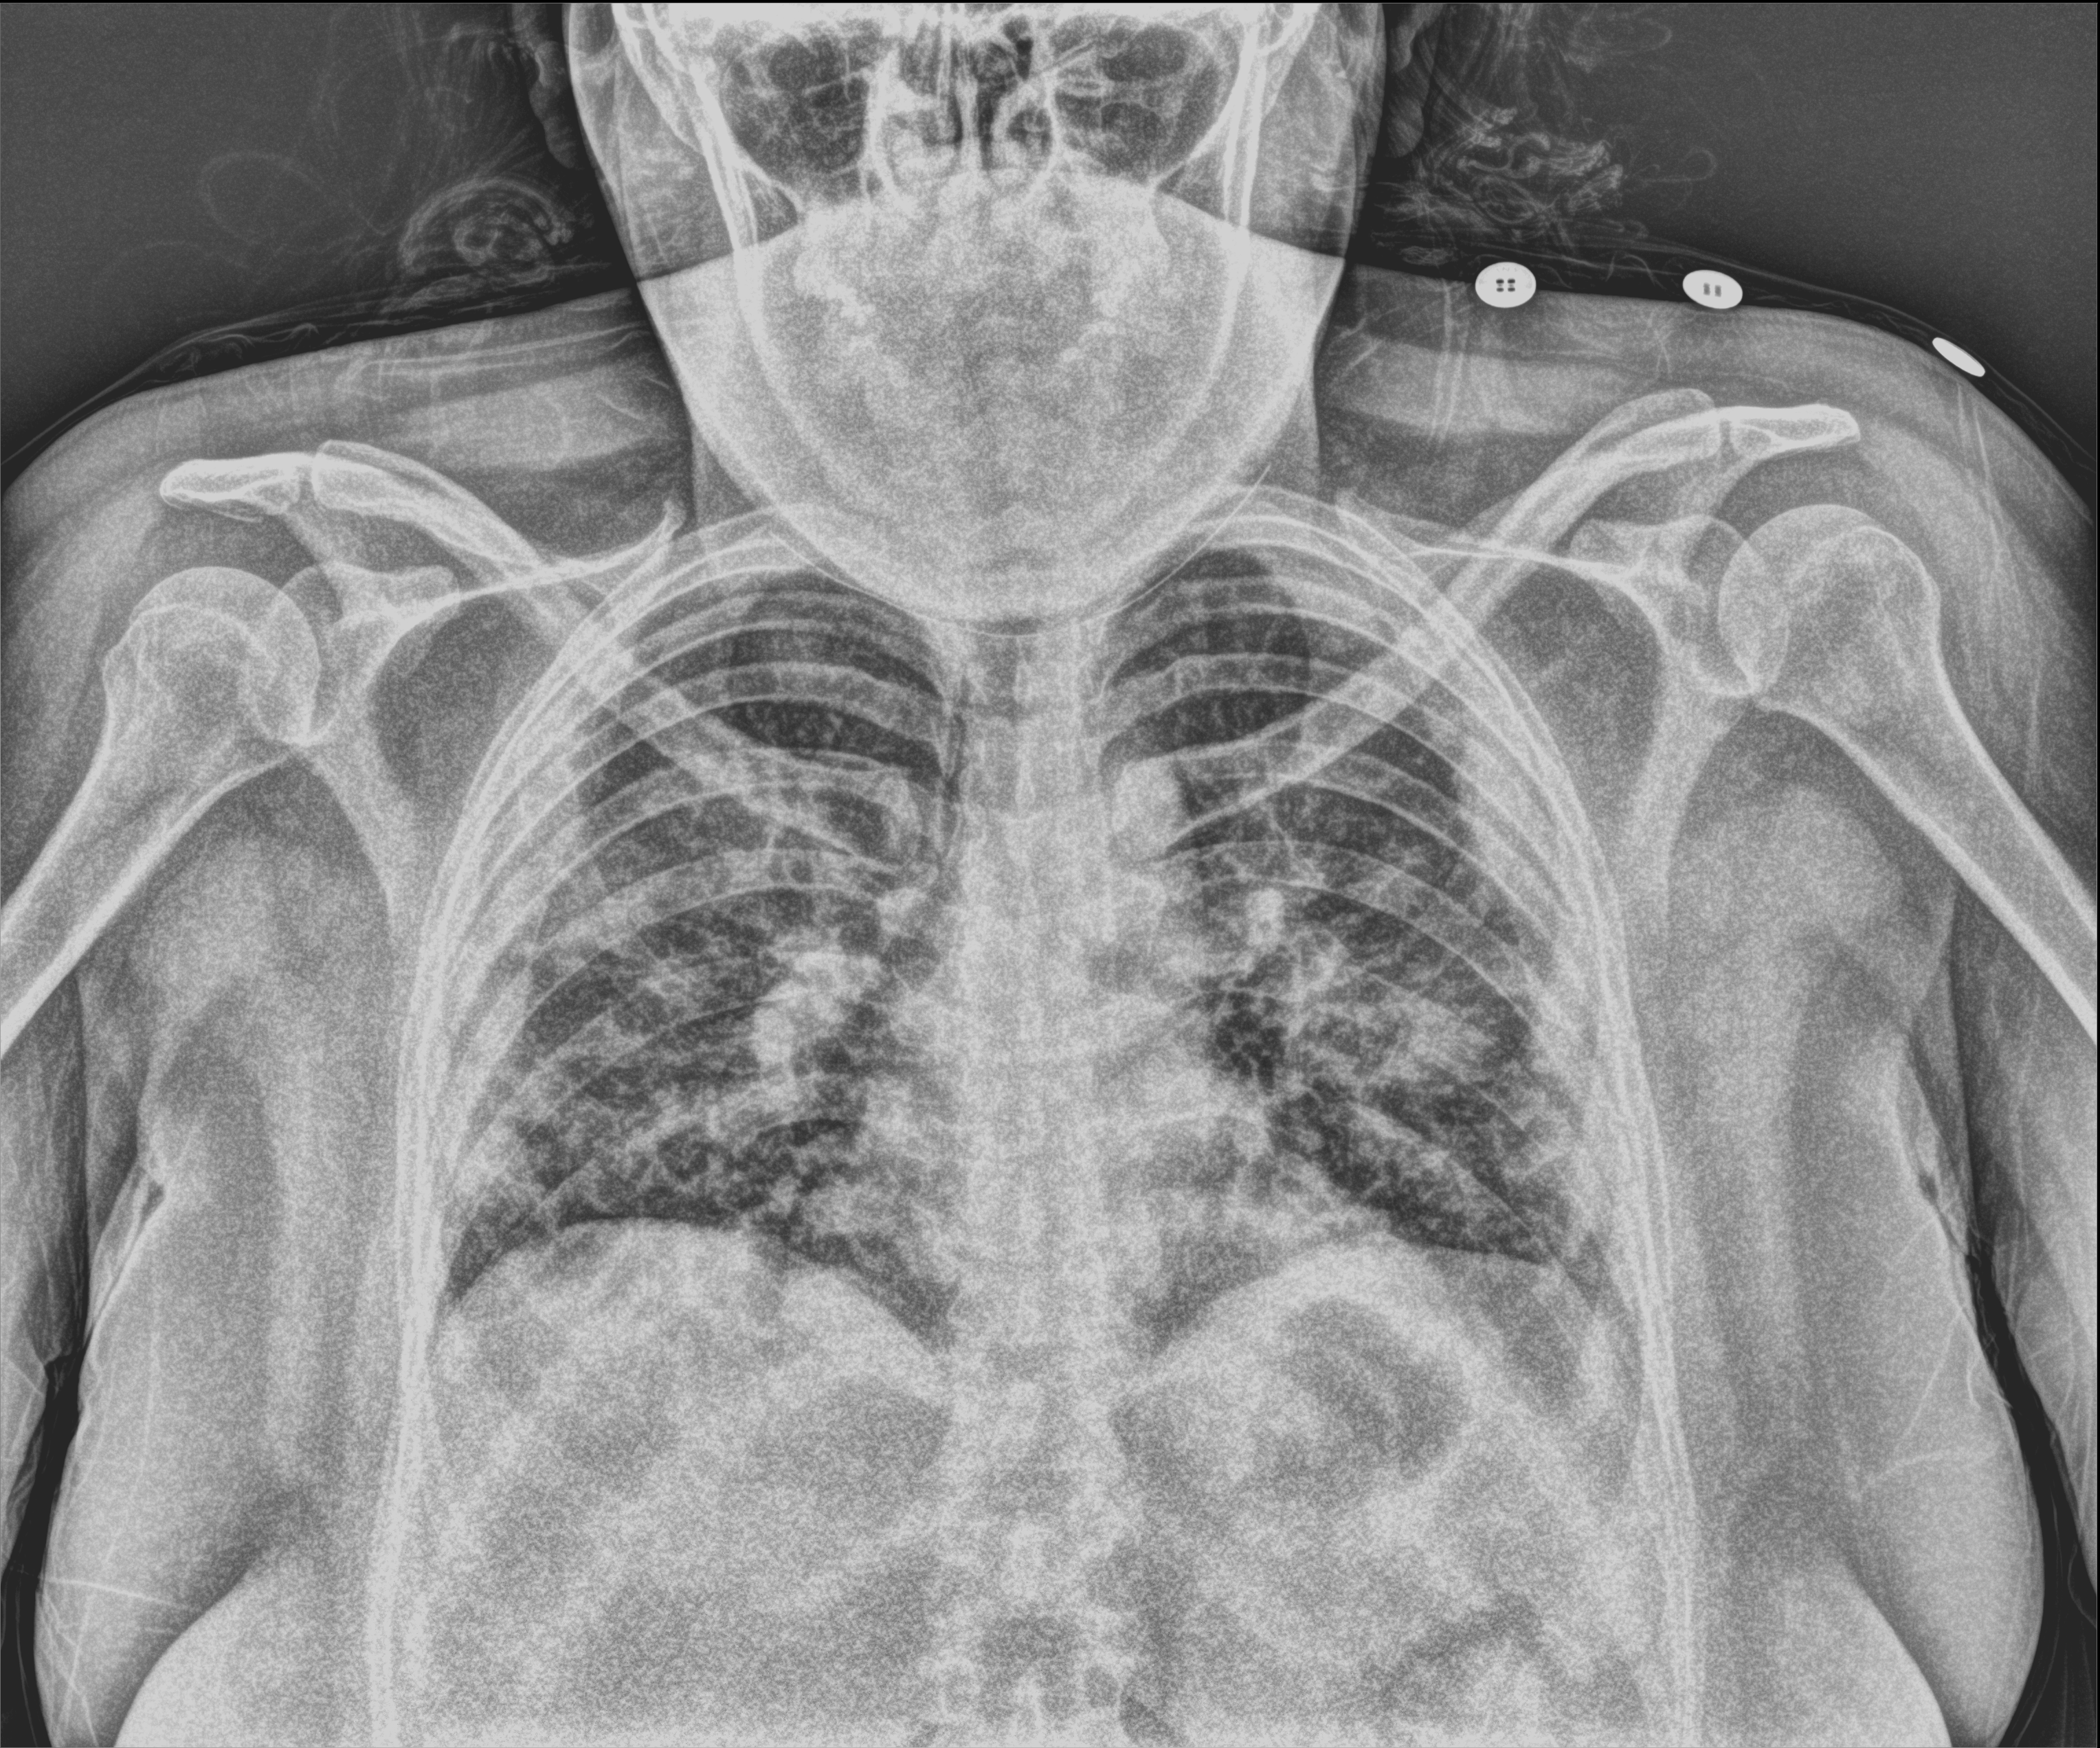
Portable chest radiograph; anteroposterior (AP) projection. Female patient hospitalised with COVID-19, age 18–59 years.
From the hospital-stay record, not from the radiograph (when in the stay this image was taken is not recorded): length of hospital stay: 3 days; admitted to intensive care during this hospital stay: no; diabetes (admission record): no.